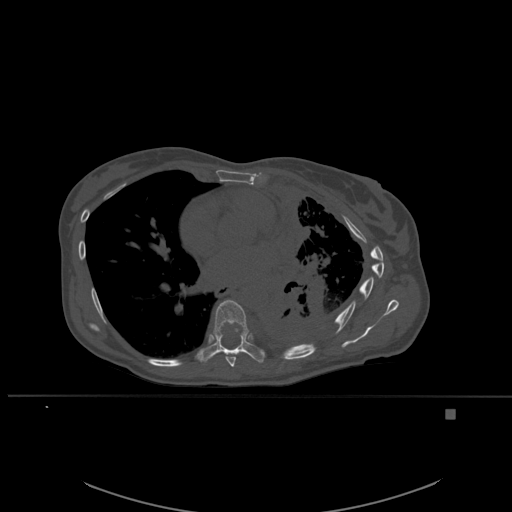
CT including the spine, one axial slice; slice 355 of 537 in the series (ordered by position); bone window (W 1800 / L 400 HU); 1.5 mm slice thickness; 512 × 512 image matrix, field of view 440 × 440 mm. Patient: female, 45 years. From the clinical record (not read from this slice): primary cancer: lung.
Structures marked on this image (semi-automatic segmentation, software-assisted and operator-edited):
- T7 vertebra: bounding box [x1, y1, x2, y2] px = [225, 356, 236, 367]
- T8 vertebra: [196, 300, 265, 363]